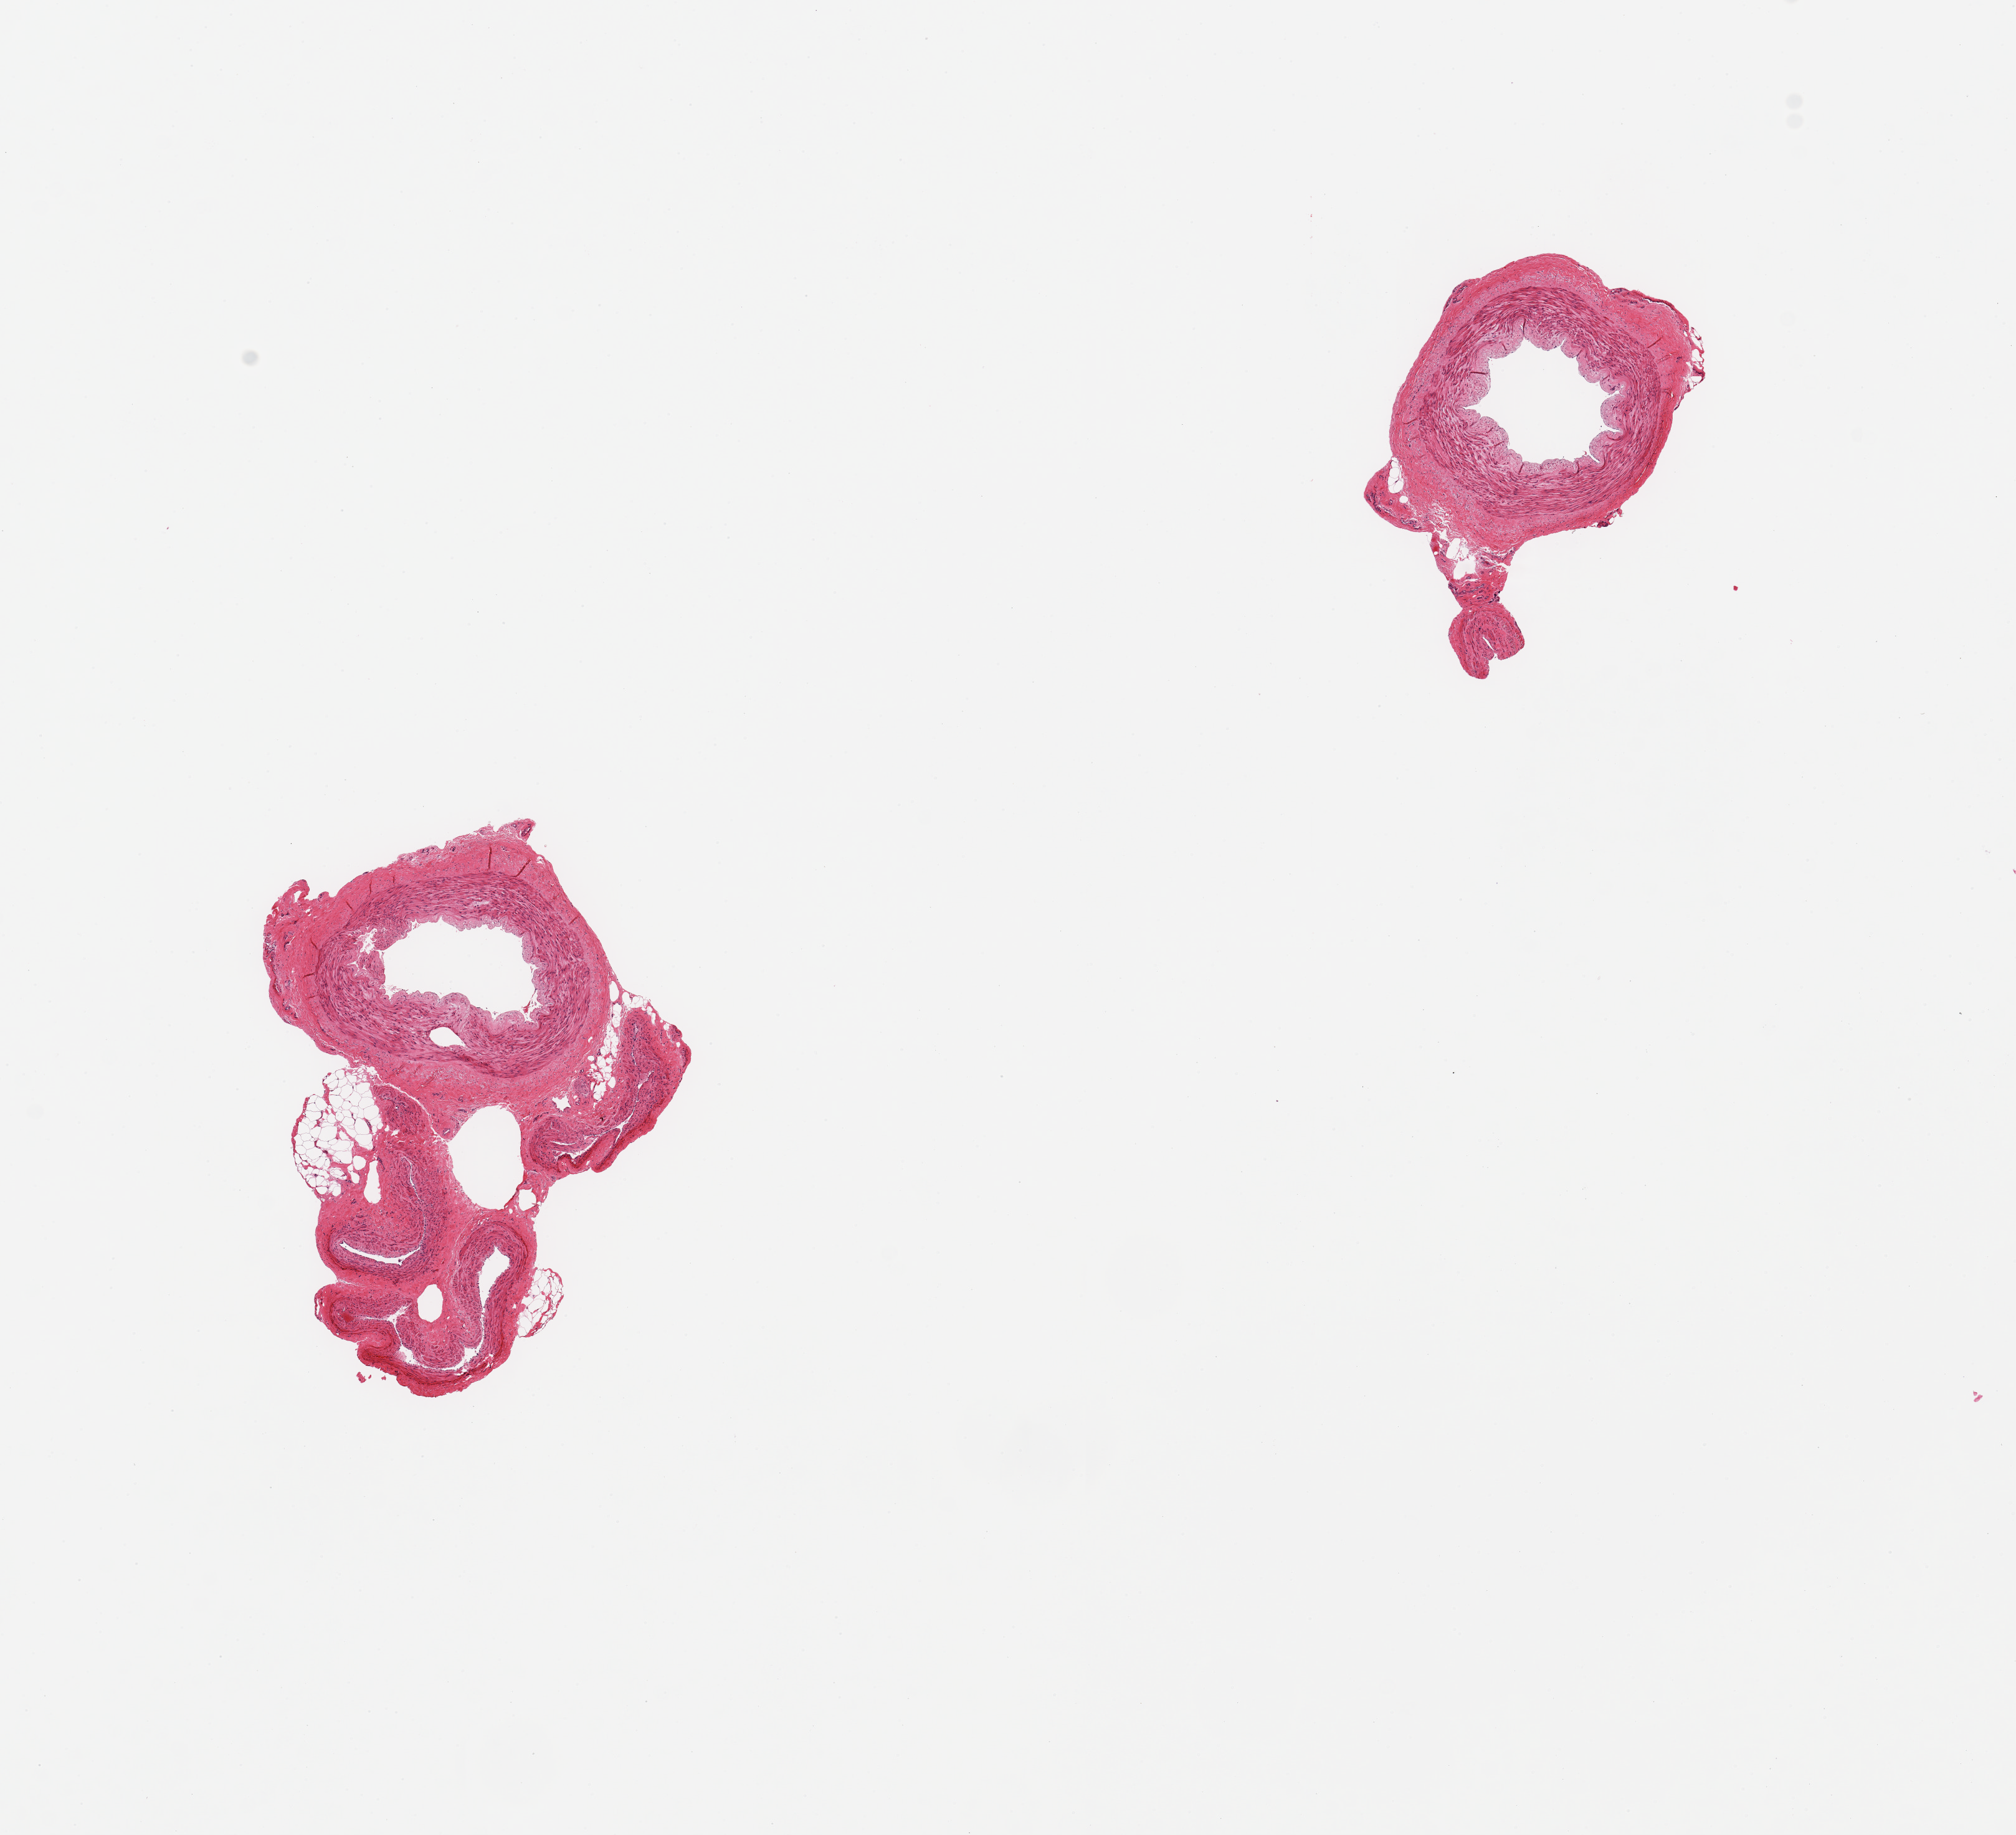
Haematoxylin and eosin whole-slide image, brightfield — low-resolution overview of the scanned area, about 12.8 x 11.7 mm; PAXgene-fixed, paraffin-embedded tissue; target tissue: tibial artery; tissue donor sample. Female donor.
- pathologist's review note for this sample: 2 pieces; well trimmed